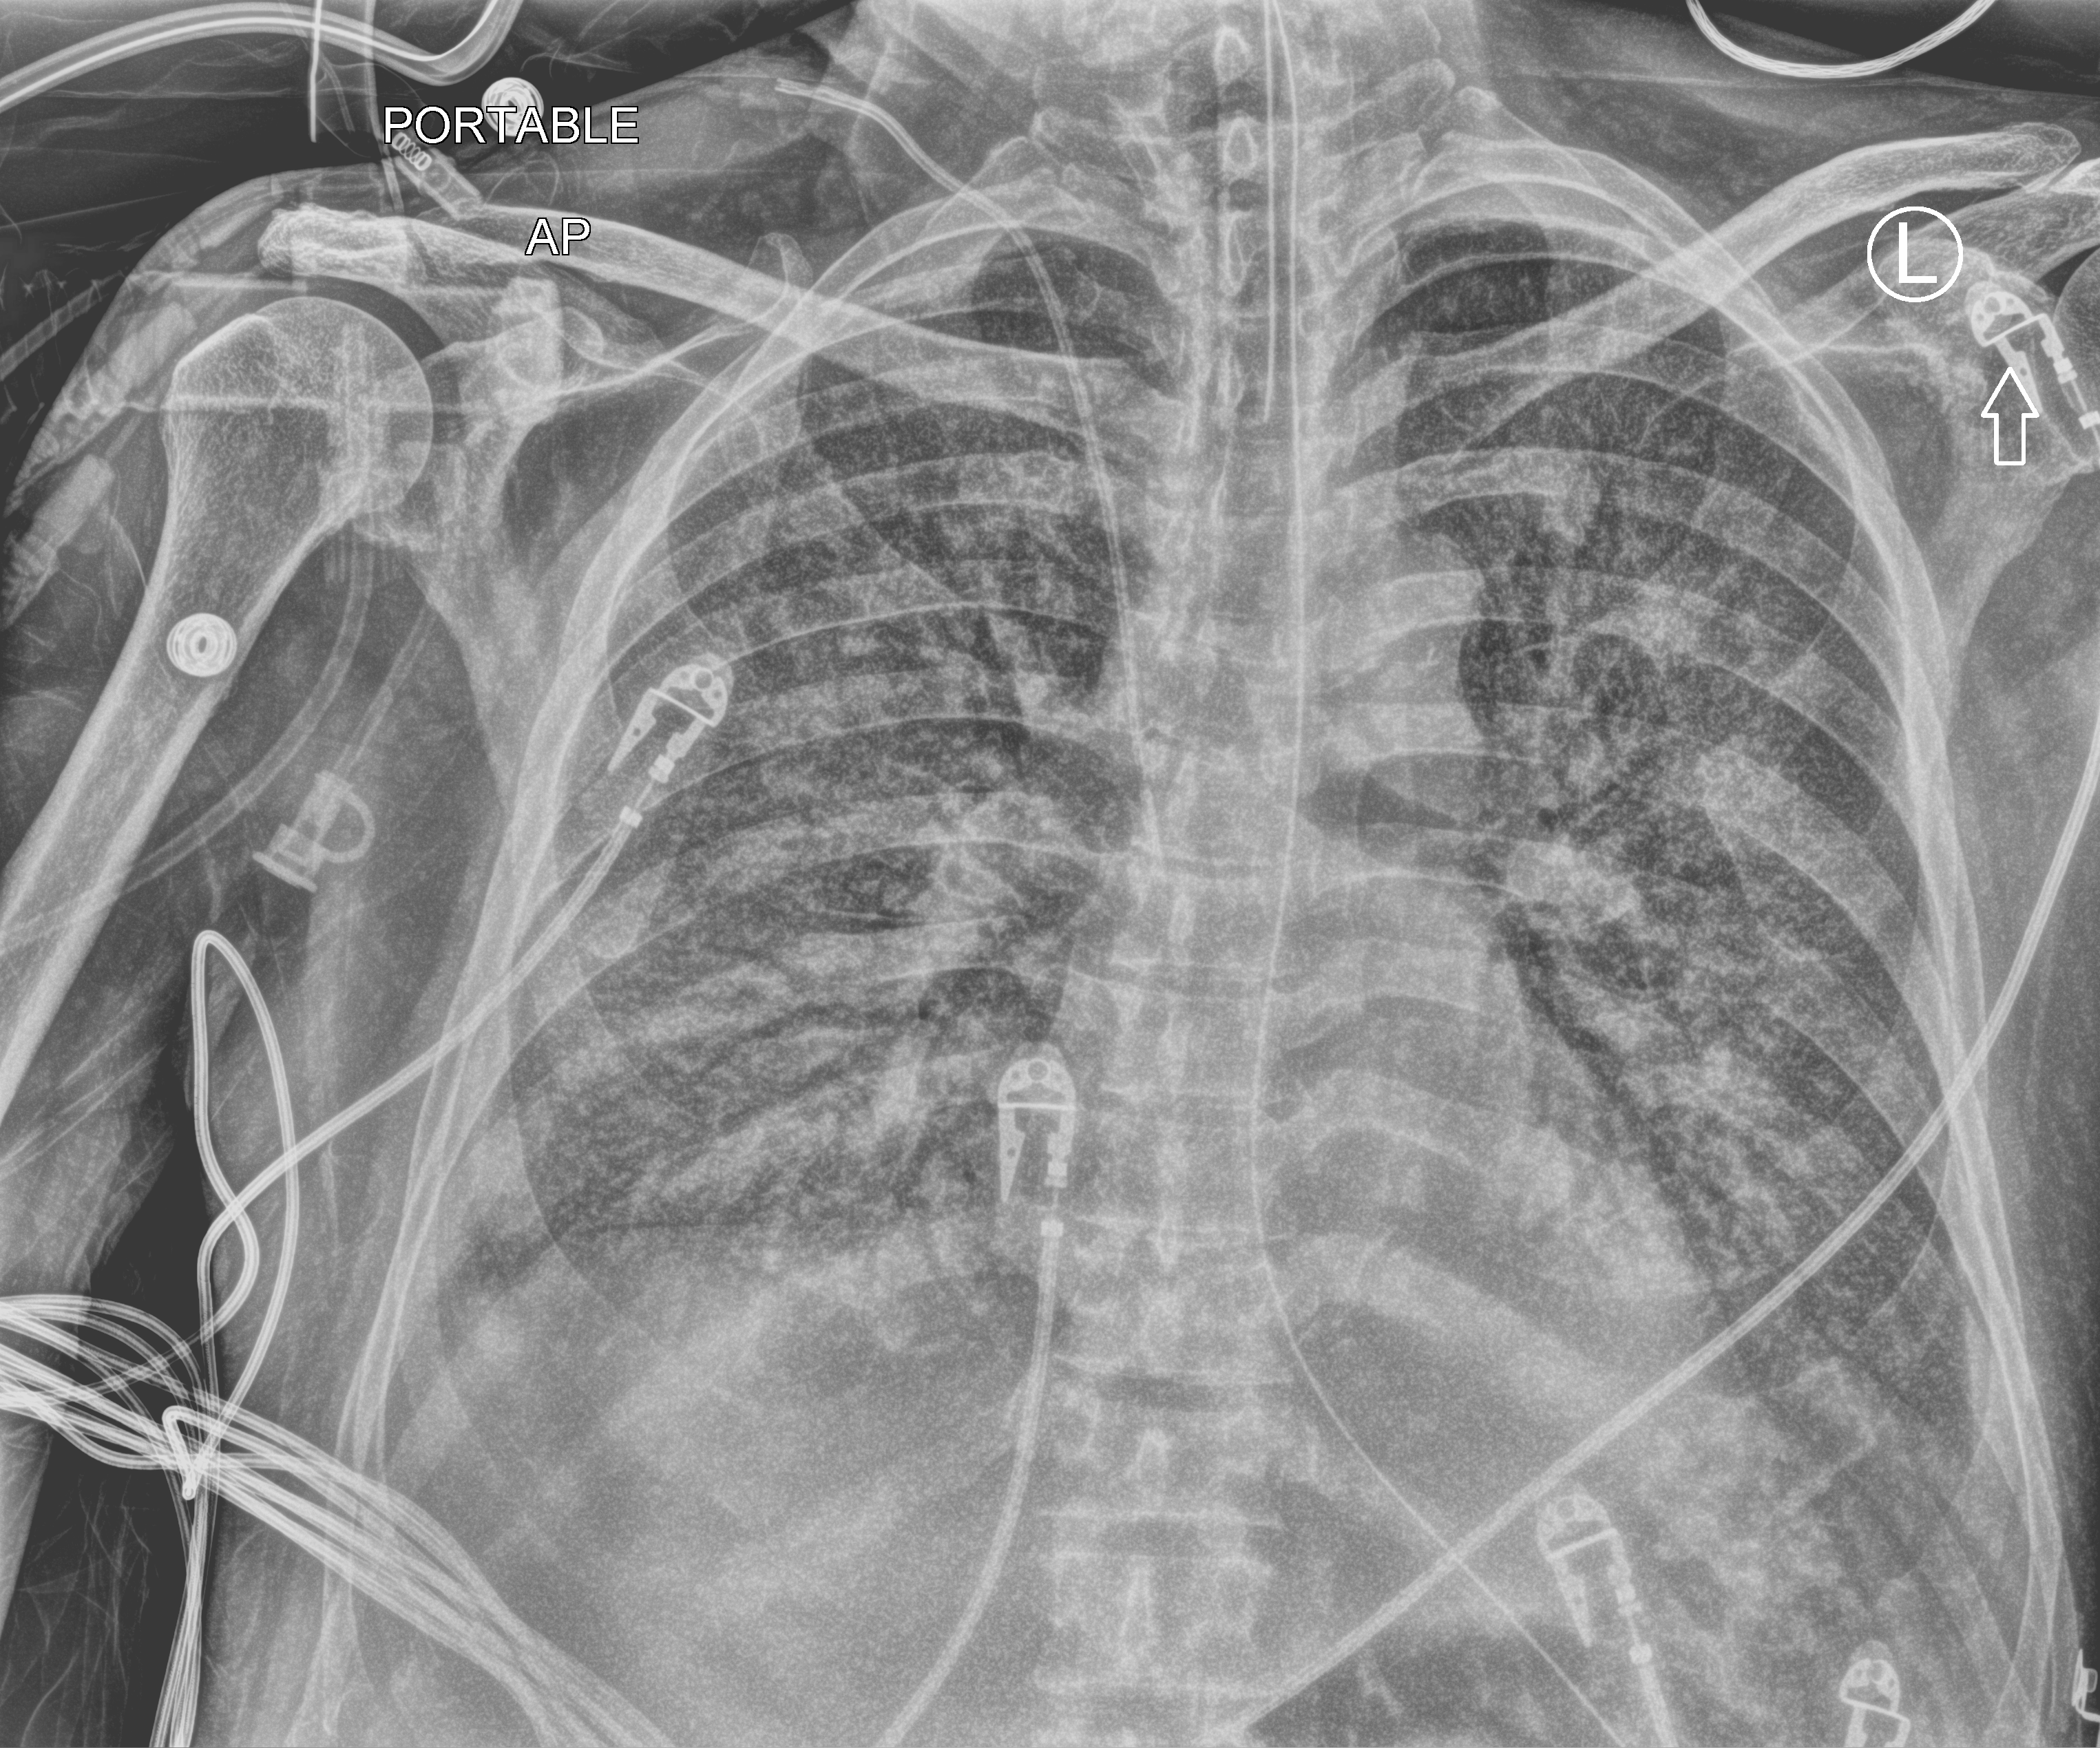
Portable chest radiograph; anteroposterior (AP) projection. Patient hospitalised with COVID-19; male, aged 60–74 years.
Admission-level facts for this patient (not findings on this image; timing relative to this image not recorded):
- smoking status (admission record): former
- chronic kidney disease (admission record): no
- length of hospital stay: 24 days